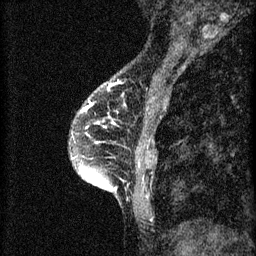
Breast MRI (dynamic contrast-enhanced), one sagittal slice; position 19 of 60 along the scan axis; 3 images stored at this slice position (order not interpretable as contrast timing); 1.5 T; TE 4.2 ms, TR 8.2 ms; 2 mm slice thickness; 256 × 256 image matrix. Patient: female, 45 years.
Outlined on this slice (semi-automatically segmented with operator editing):
- analysis volume of interest (the breast-tissue region the enhancement analysis was run in; not a lesion): bounding box <72,104,157,217> (left, top, right, bottom; pixels)
- tumour enhancement mask (voxels above the 70 % enhancement threshold inside the analysis volume of interest): <82,106,117,191>